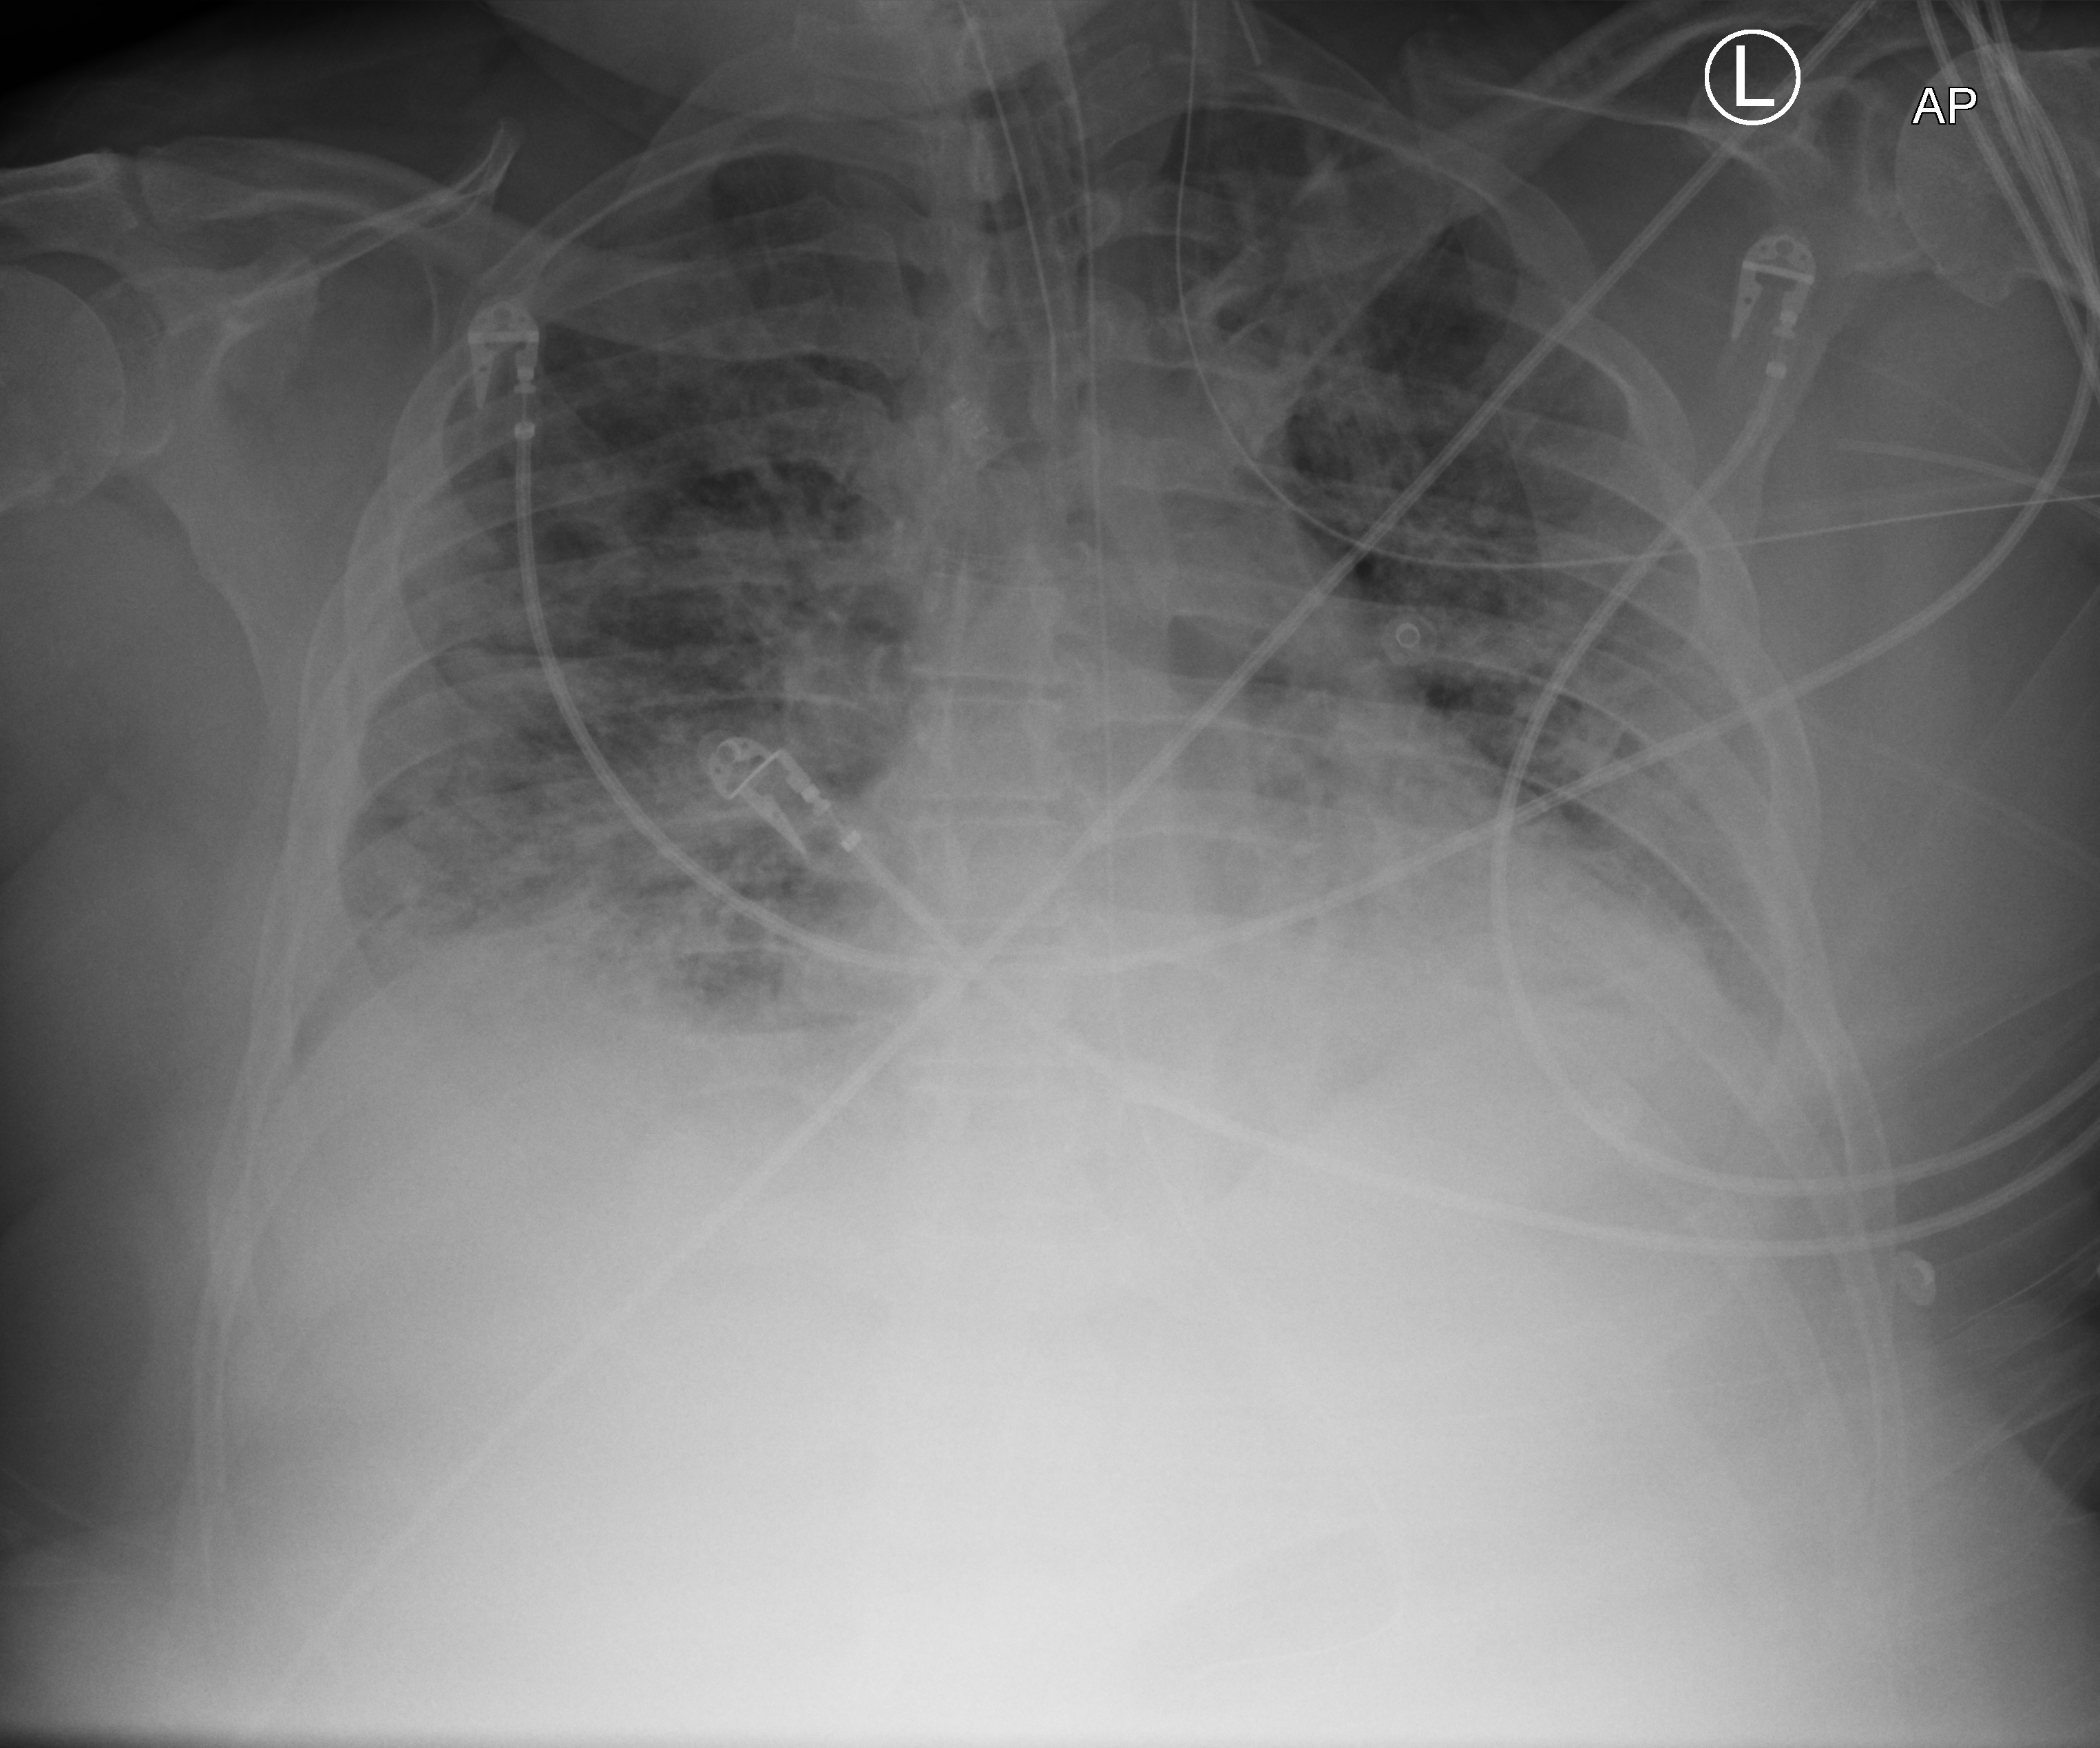
Portable chest radiograph; anteroposterior (AP) projection. Male patient hospitalised with COVID-19, age 18–59 years.
Admission-level facts for this patient (not findings on this image; timing relative to this image not recorded):
- hypertension (admission record): yes
- chronic kidney disease (admission record): no